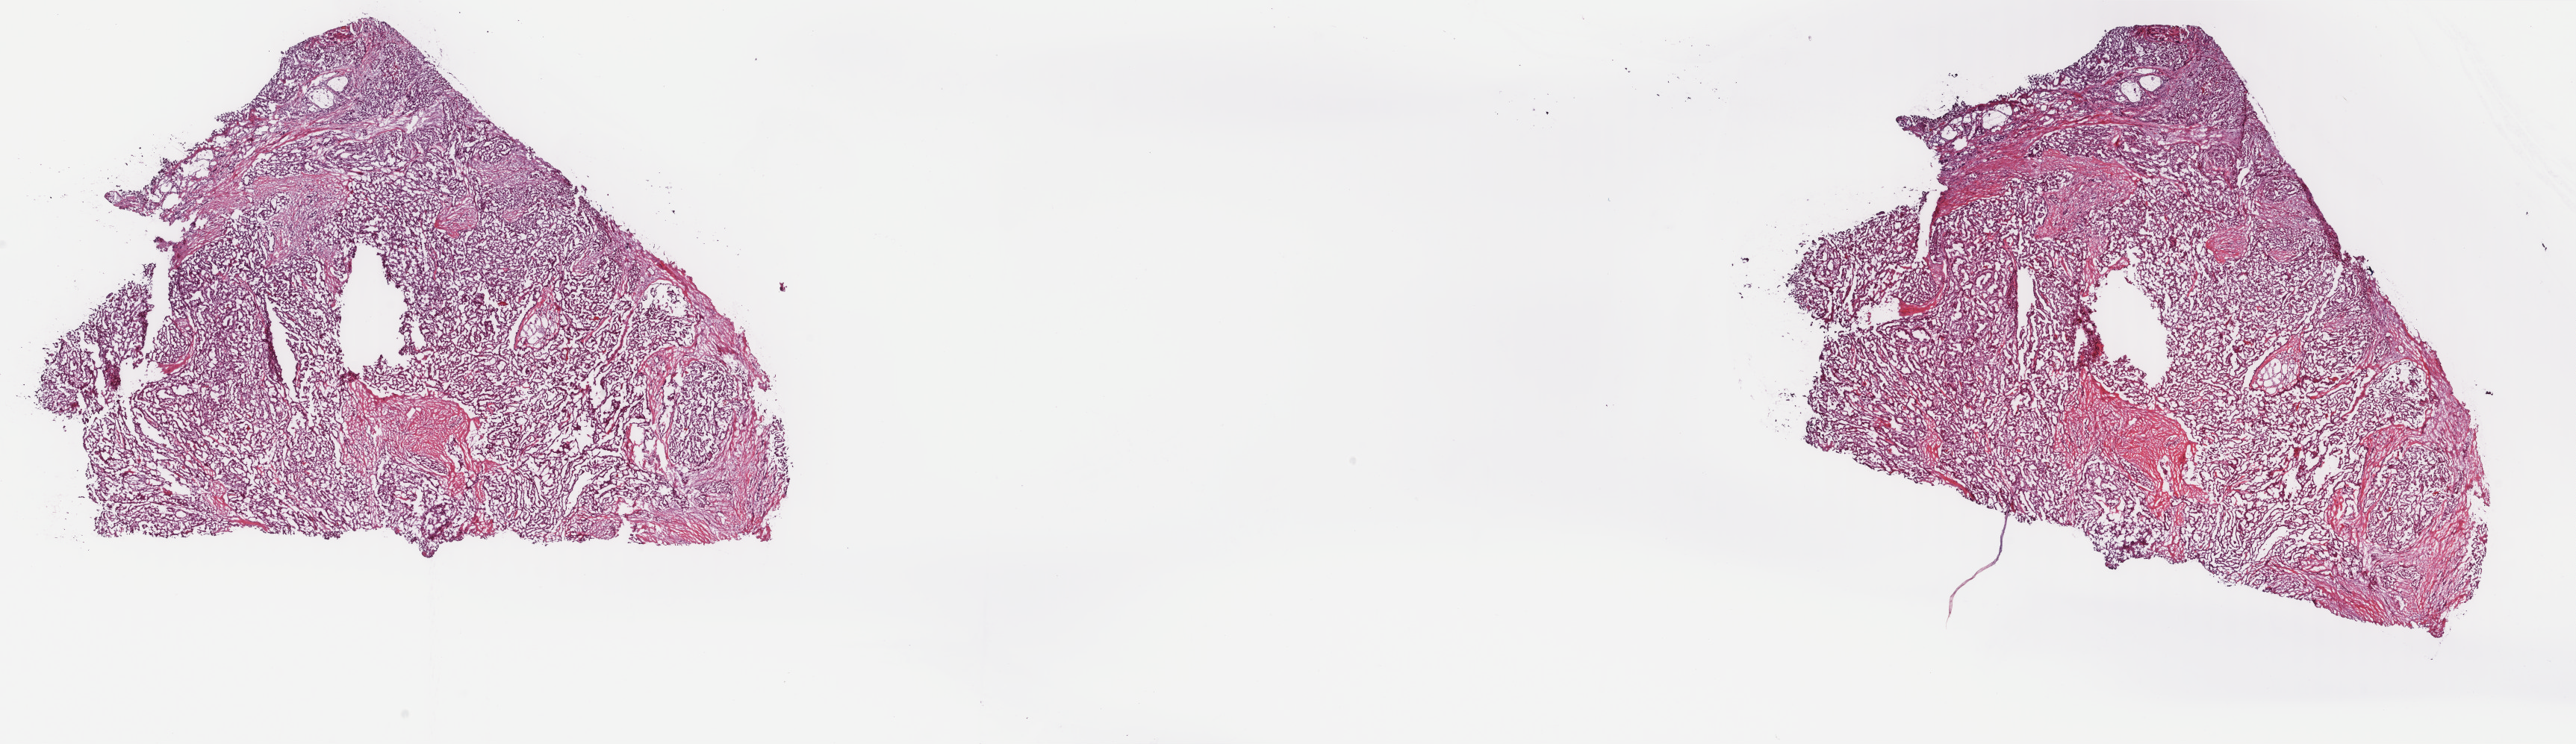
Hematoxylin and eosin (H&E) stained whole-slide image, low-resolution overview of the scanned area, about 27.4 x 7.9 mm (from a 40x scan), frozen section from the top of the tissue portion, sample: primary tumour, thyroid. Patient: male, age at initial diagnosis 54 years. Slide review estimates, as recorded: tumour cells 80%, tumour nuclei 100%, normal cells 0%, stromal cells 20%, necrosis 0%. Infiltration values recorded for this section: lymphocyte infiltration 0%, monocyte infiltration 0%, neutrophil infiltration 0%.
- histologic diagnosis: Papillary carcinoma, columnar cell (thyroid gland)
- TNM: T3 N0 M0
- AJCC pathologic stage: III (7th edition)